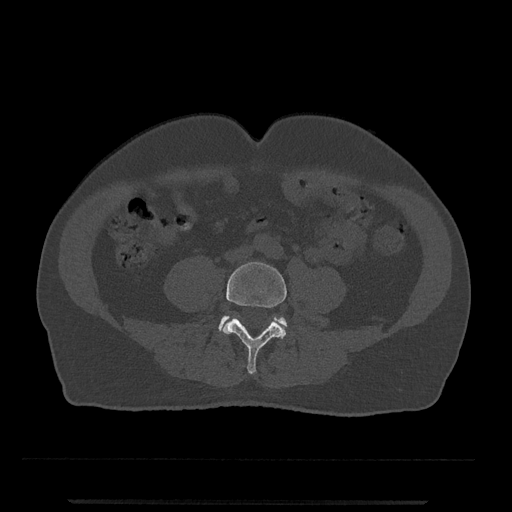
CT including the spine, one axial slice. Position 121 of 797 along the scan axis. 120 kVp. Bone window (W 1800 / L 400 HU). 0.5 mm slice thickness. 512 × 512 image matrix, field of view 419 × 419 mm. Patient: male, 63 years. Case-level facts recorded for this patient, not image findings: primary cancer: prostate.
Annotated regions visible in this slice (semi-automatic segmentation, software-assisted and operator-edited):
- L4 vertebra: bounding box (x1, y1, x2, y2) in pixels: (222, 262, 287, 375)
- L5 vertebra: (218, 316, 287, 332)